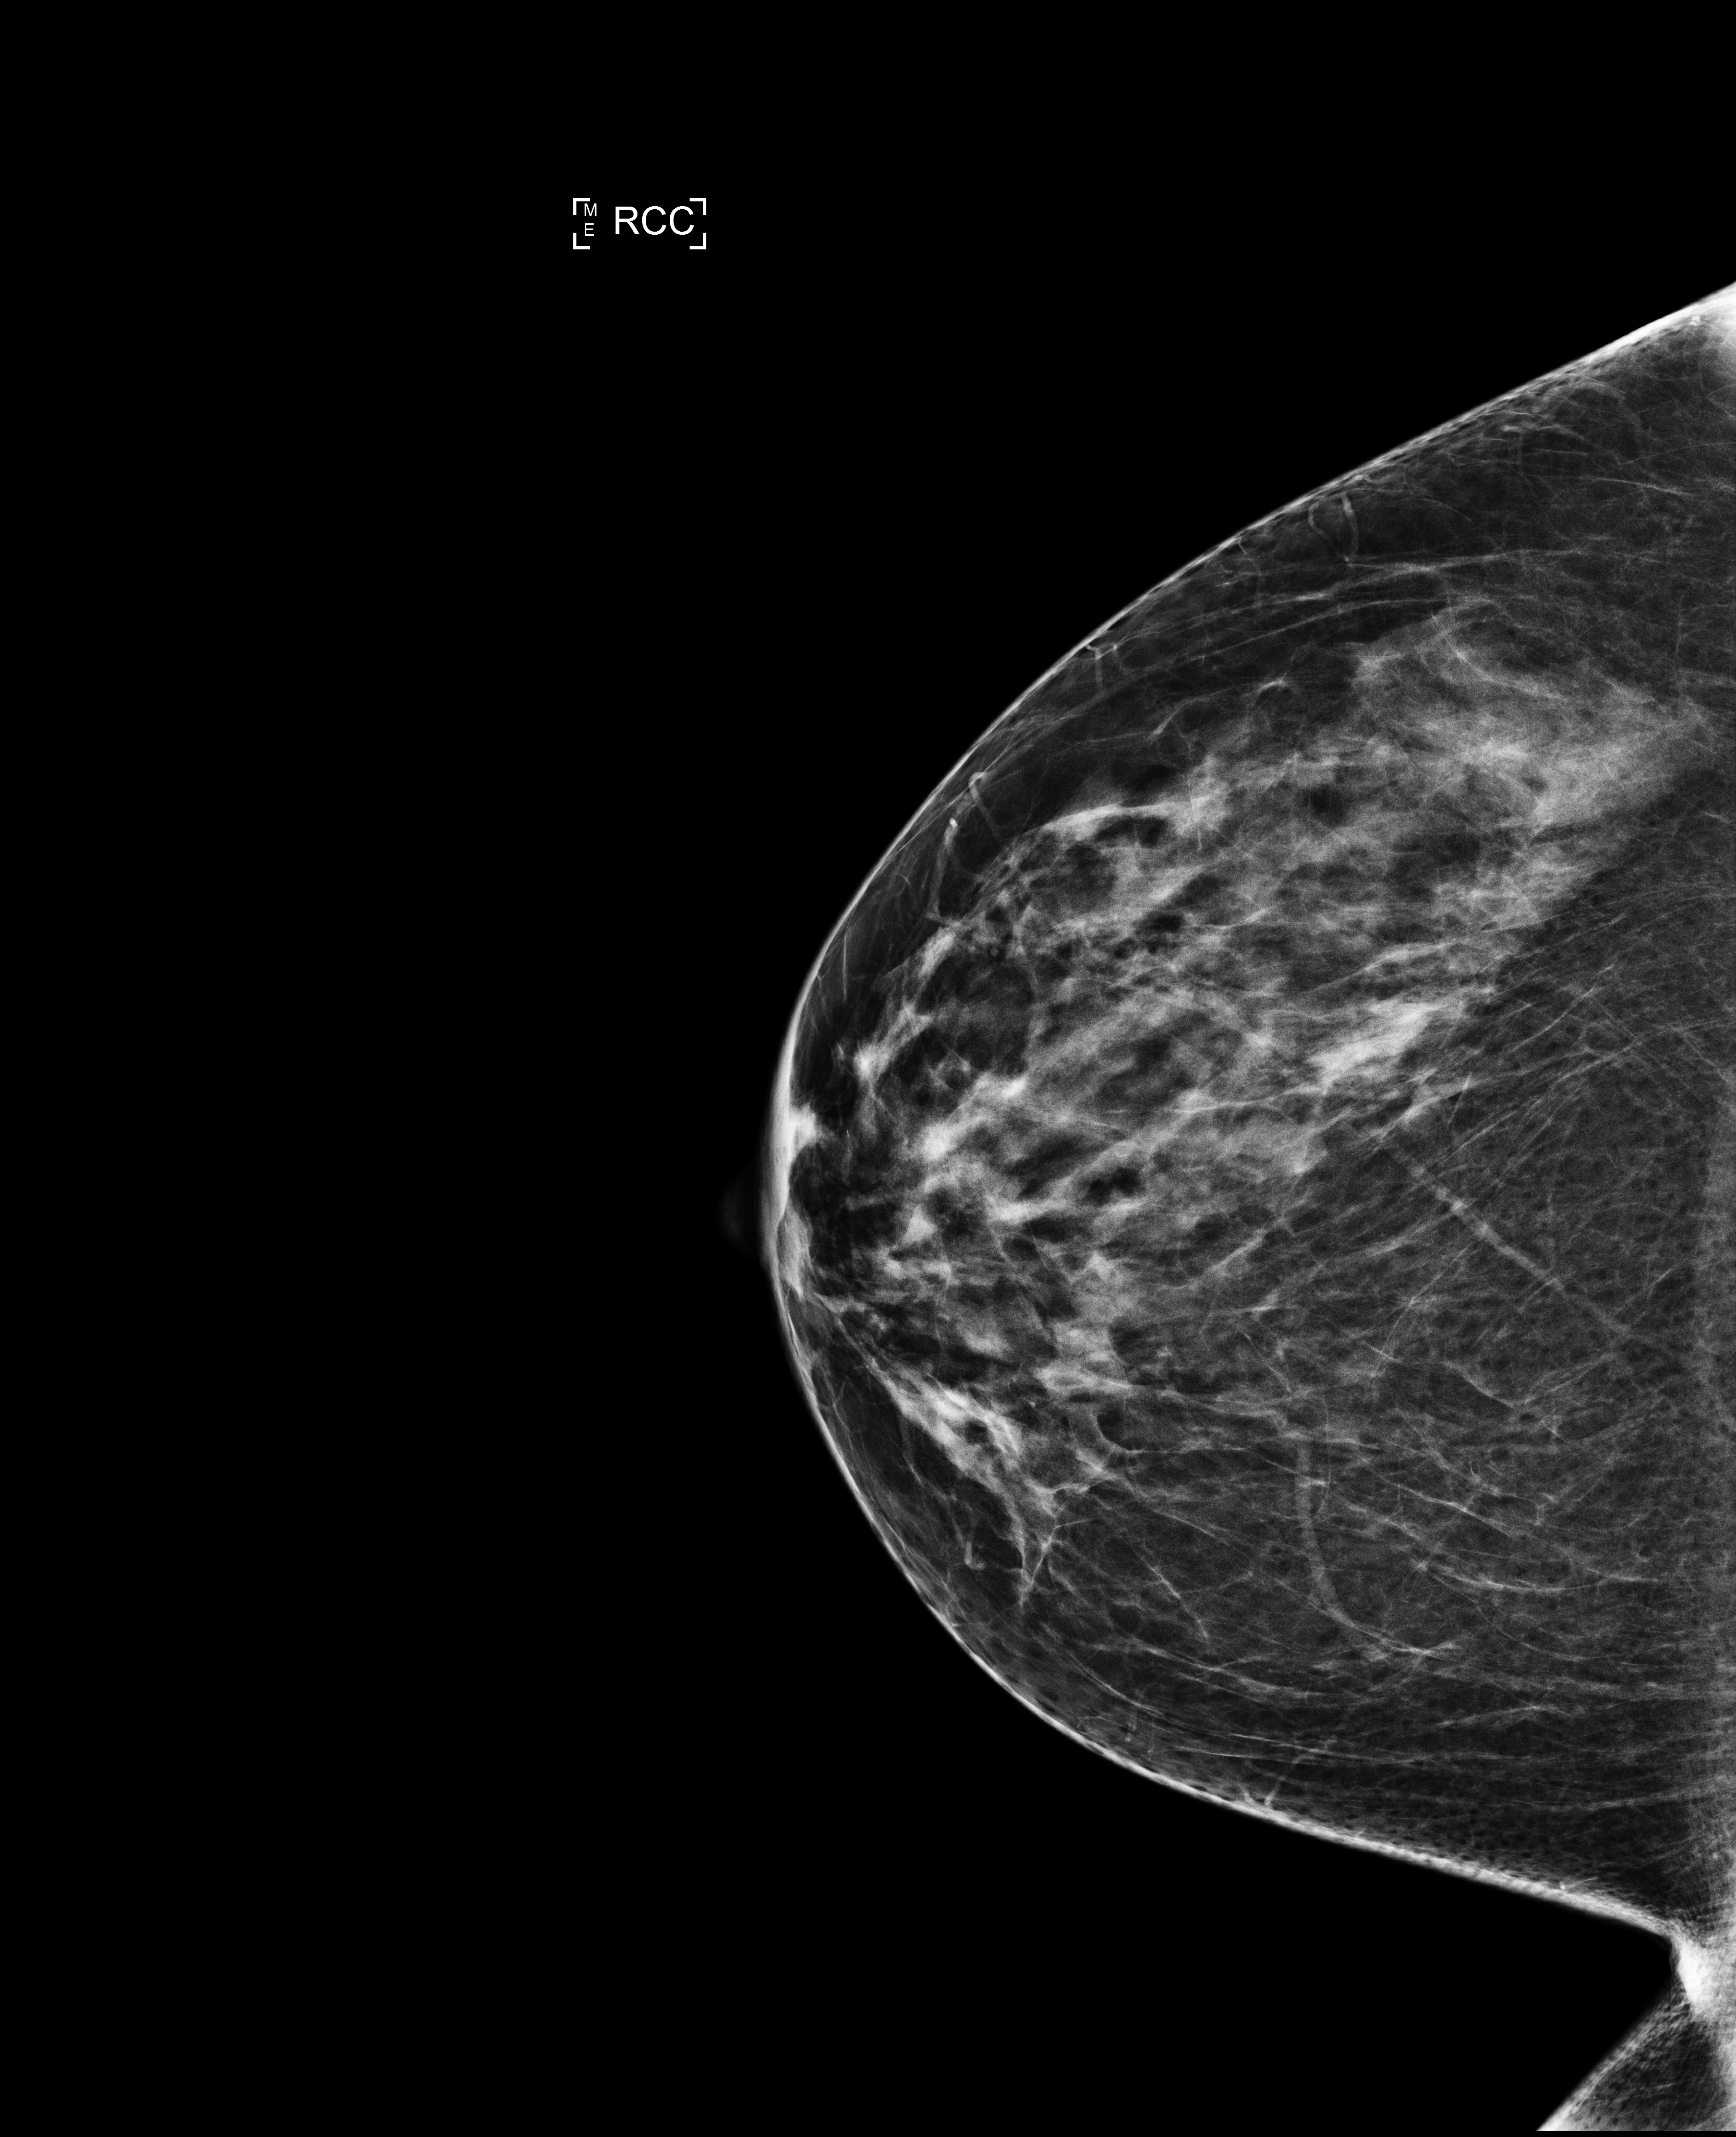
Annual screening mammography examination; system: Selenia Dimensions. Patient: female, 52 years.
Image type: full-field digital mammogram. Breast: right. Projection: cranio-caudal projection.